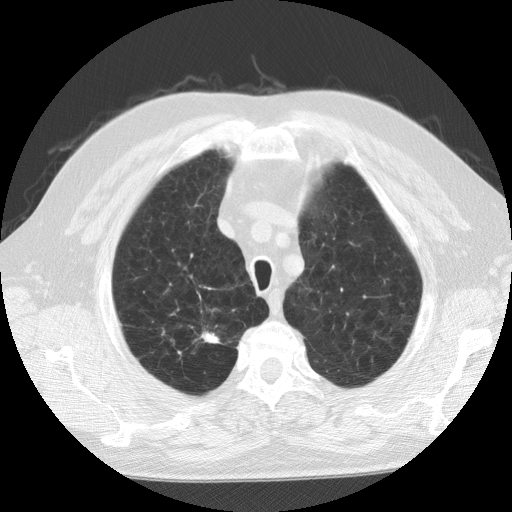
Axial slice from a low-dose chest CT screening exam. Second screening round (one year after baseline). Lung window (W 1500 / L -600 HU). Standard (soft-tissue) reconstruction kernel (STANDARD). Slice 20 of 109 in the series. Male, age 64 years at enrolment.
Lesion marked by an expert reader, box from (x=185, y=320) to (x=236, y=358) px. The screening reader recorded 2 non-calcified nodules or masses ≥4 mm on this exam; which of them this box marks is not recorded. Official screen result: positive, other. Lung cancer was diagnosed 233 days after this screen: squamous cell carcinoma, NOS, left upper lobe, moderately differentiated (G2), stage IA (AJCC 6th edition), 10 mm at pathology.